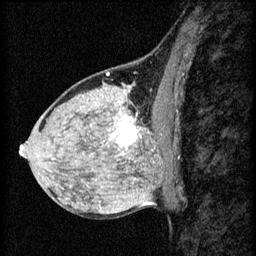
Breast MRI (dynamic contrast-enhanced), one sagittal slice; position 30 of 60 along the scan axis; 3 images stored at this slice position (order not interpretable as contrast timing); 1.5 T; TE 4.2 ms, TR 8.2 ms; 2 mm slice thickness; 256 × 256 image matrix. Female patient, age 40 years.
Outlined on this slice (semi-automatic segmentation, software-assisted and operator-edited):
- analysis volume of interest (the breast-tissue region the enhancement analysis was run in; not a lesion): box from (x=108, y=108) to (x=167, y=159) px
- tumour enhancement mask (voxels above the 70 % enhancement threshold inside the analysis volume of interest): (x=110, y=116)–(x=149, y=147)